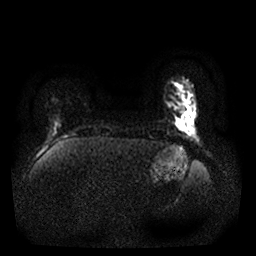
Breast MRI, one axial slice; slice 3 of 25 in the series (ordered by position); diffusion-weighted series; image 2 of 4 stored at this slice position (different b-values; order by instance number); 1.5 T; 4 mm slice thickness; 256 × 256 image matrix, field of view 290 × 290 mm. Female patient.
Structures marked on this image (outlined manually by an expert reader):
- tumour on diffusion-weighted imaging: bounding box [x1, y1, x2, y2] px = [177, 106, 186, 132]